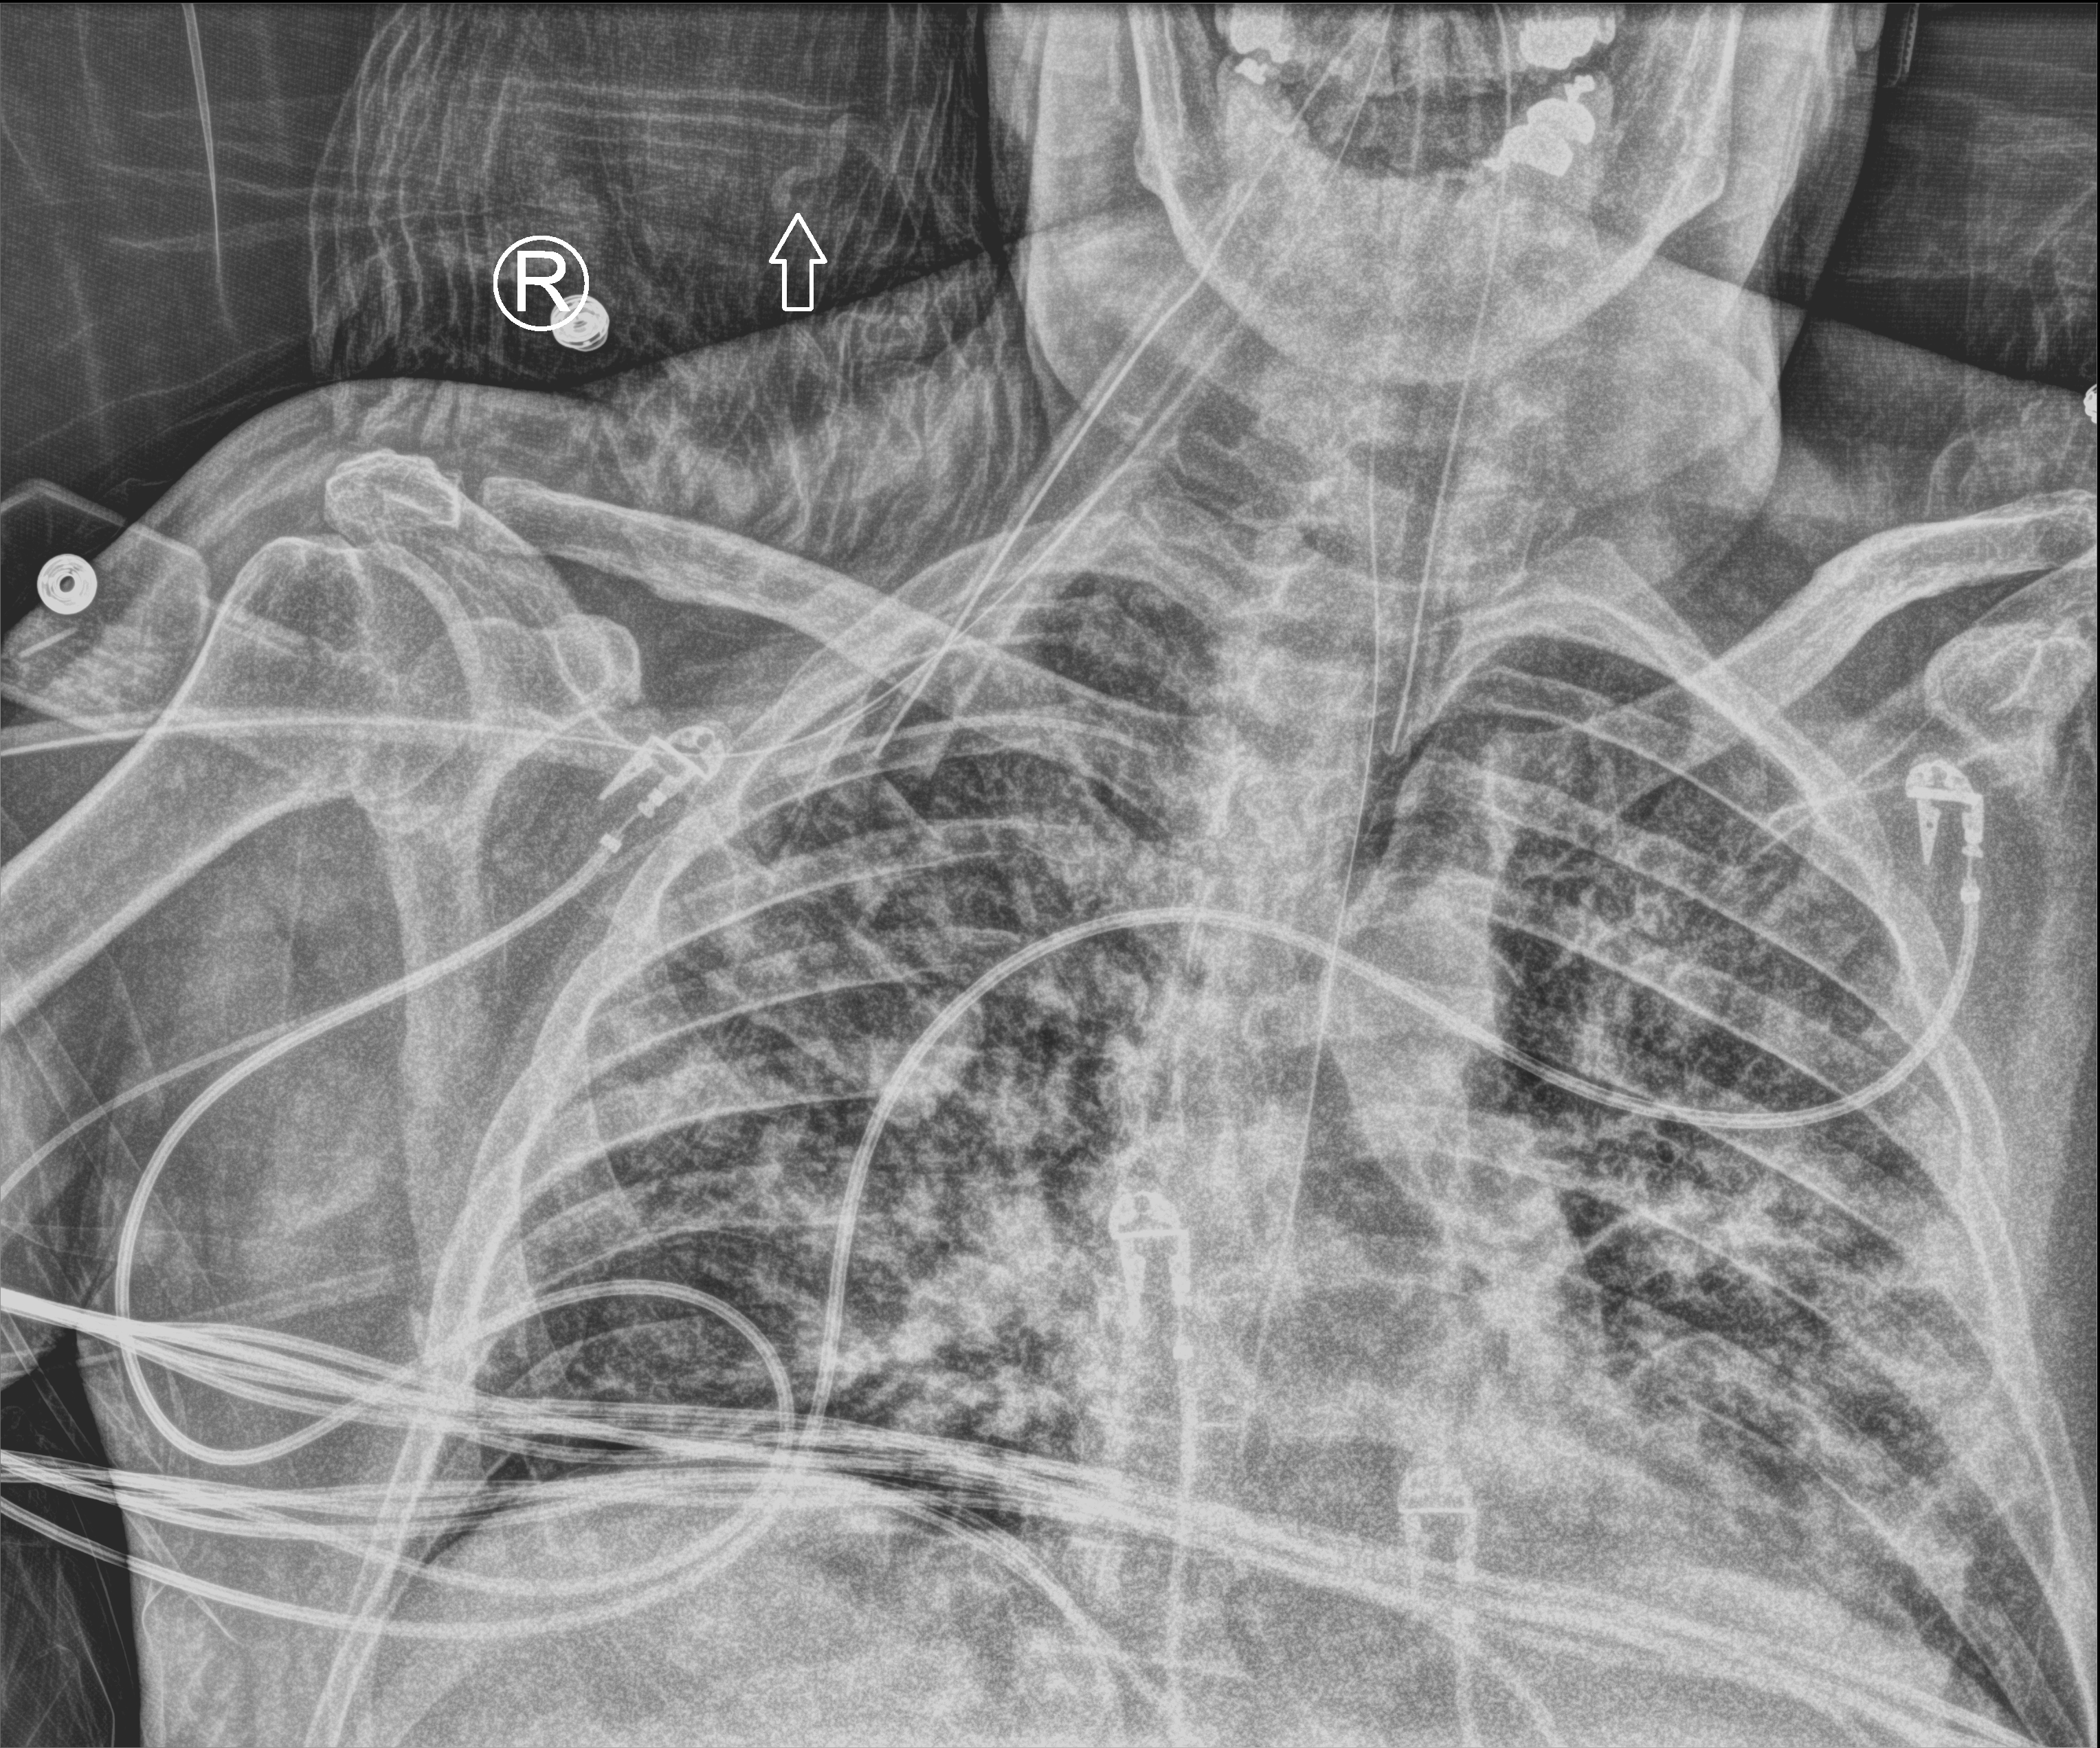
Portable chest radiograph; anteroposterior (AP) projection. Patient hospitalised with COVID-19; male, aged 60–74 years.
From the hospital-stay record, not from the radiograph (when in the stay this image was taken is not recorded): length of hospital stay: 24 days; admitted to intensive care during this hospital stay: yes; chronic kidney disease (admission record): no.